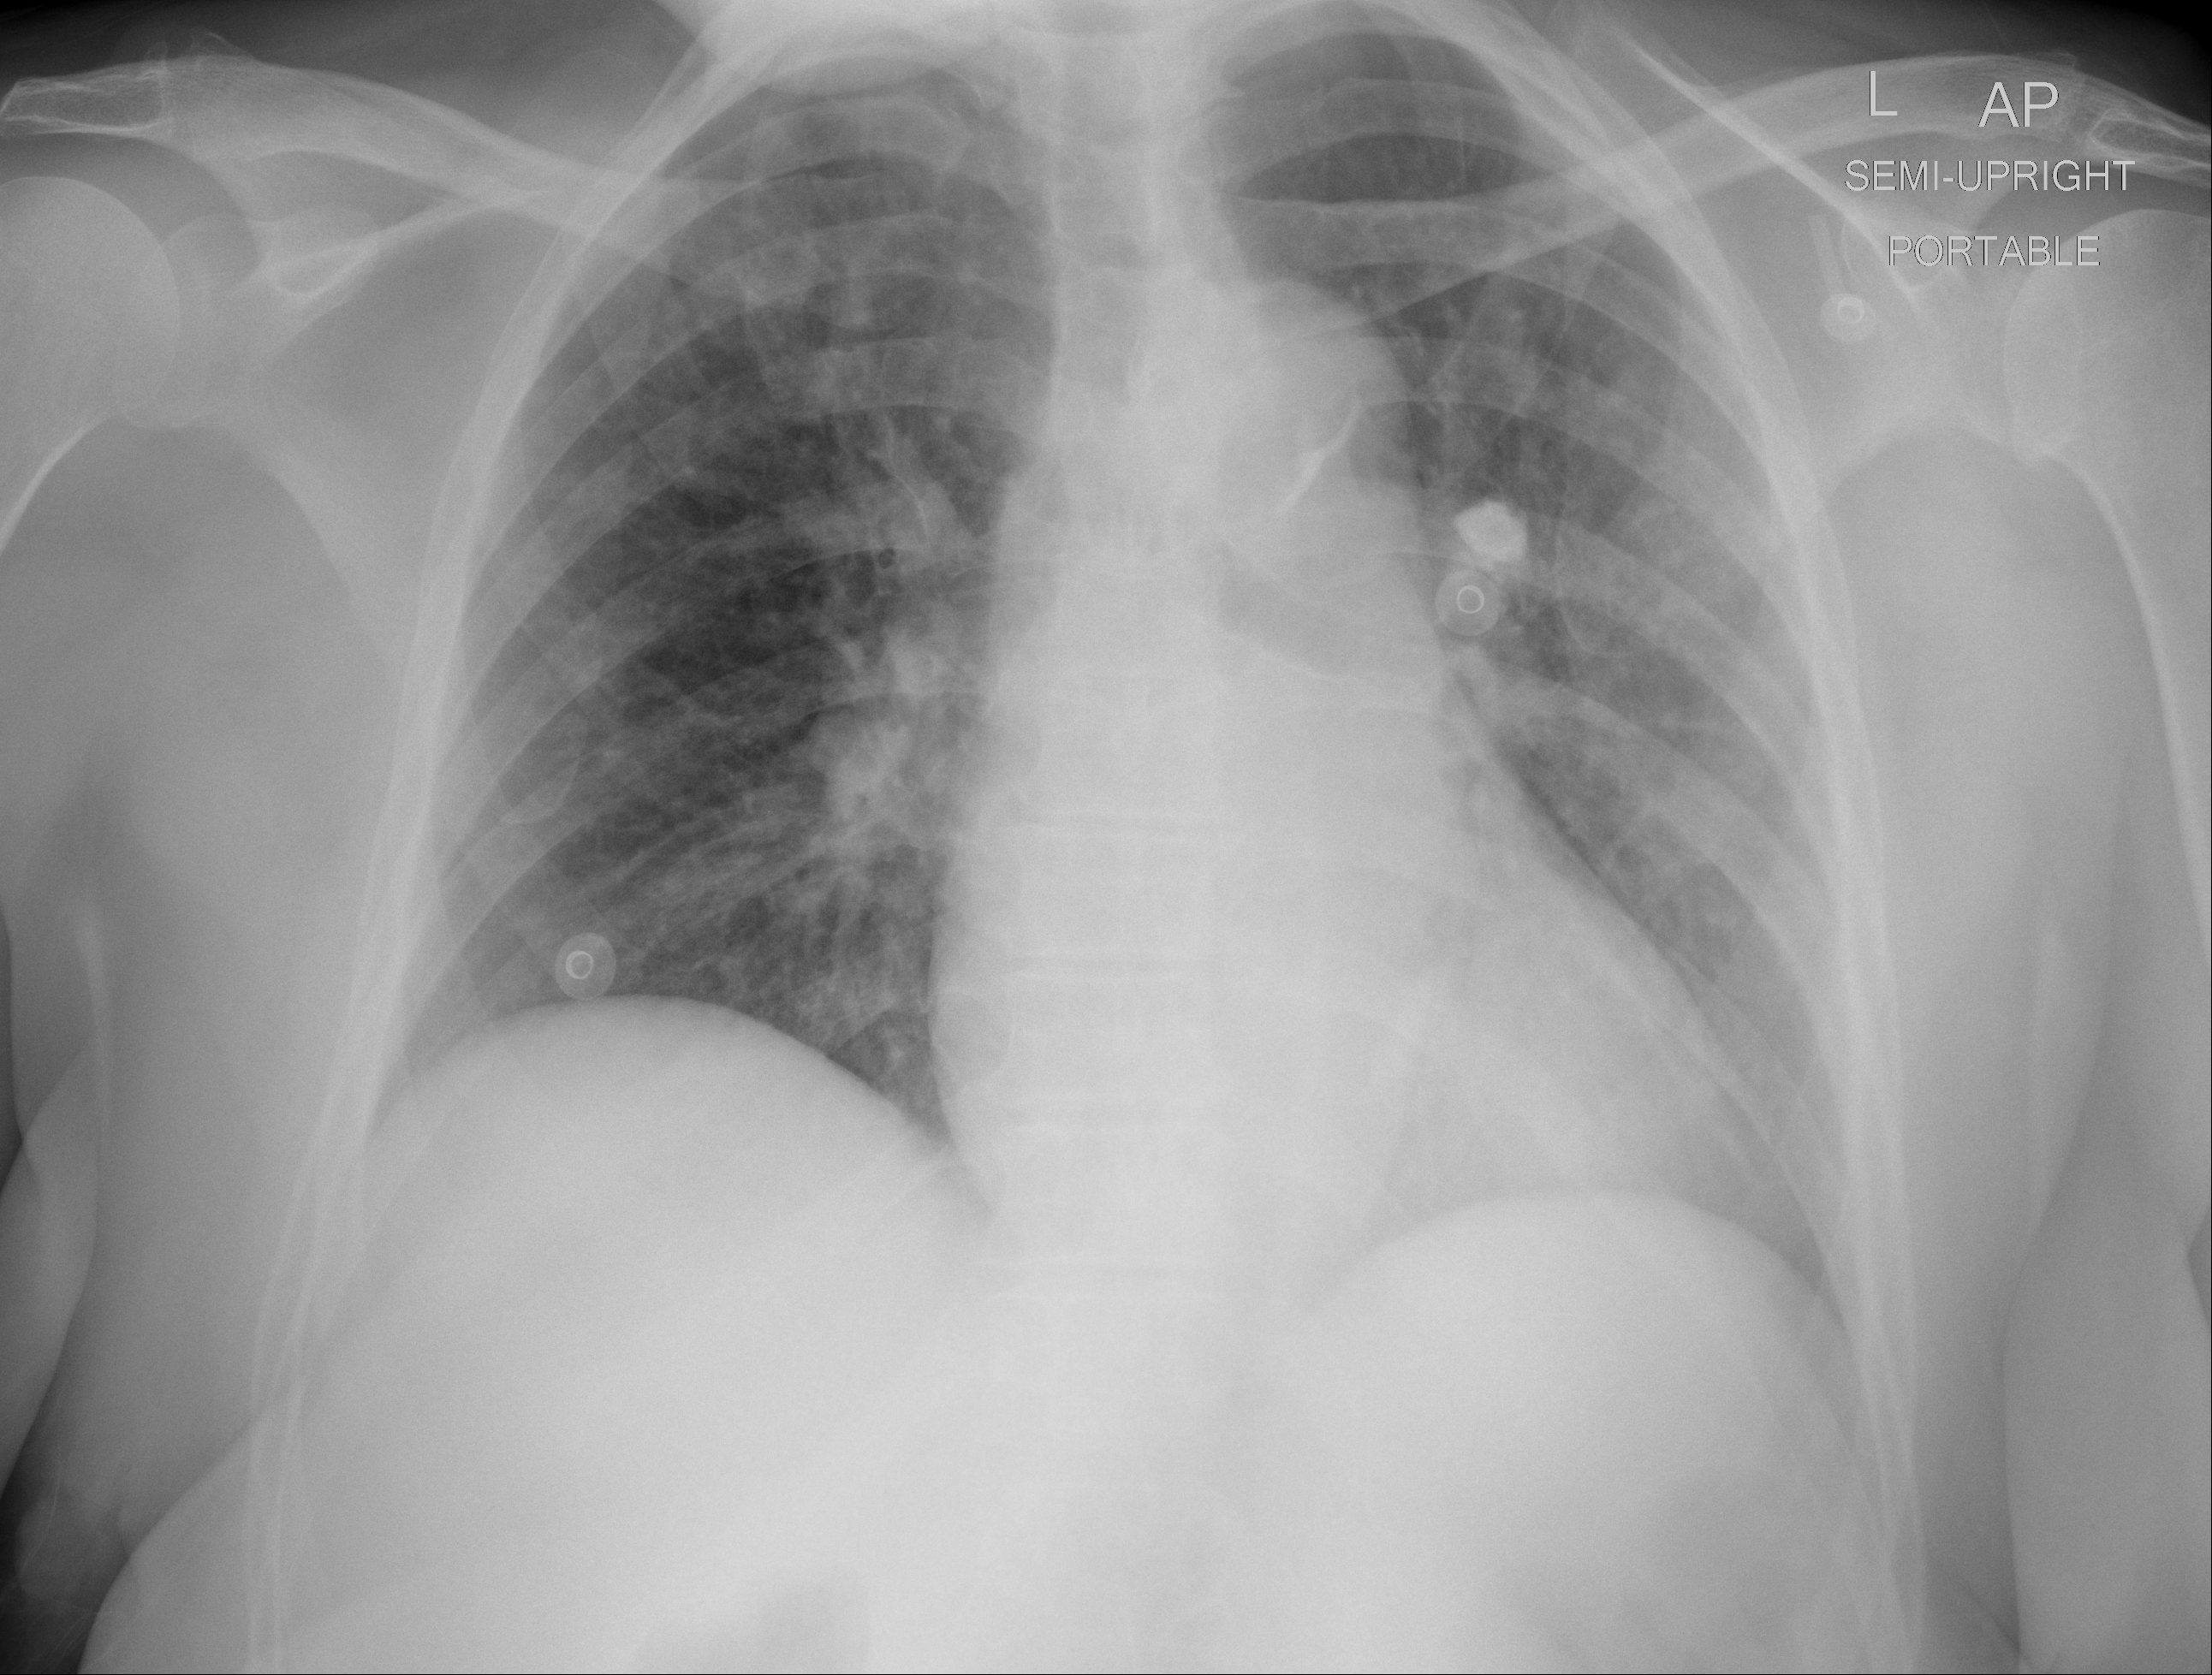
Portable chest radiograph, AP projection. Female patient, age 64 years; imaged 1 day after the COVID-19 diagnosis.
Key findings recorded by the radiologist: No definite acute cardiopulmonary findings.